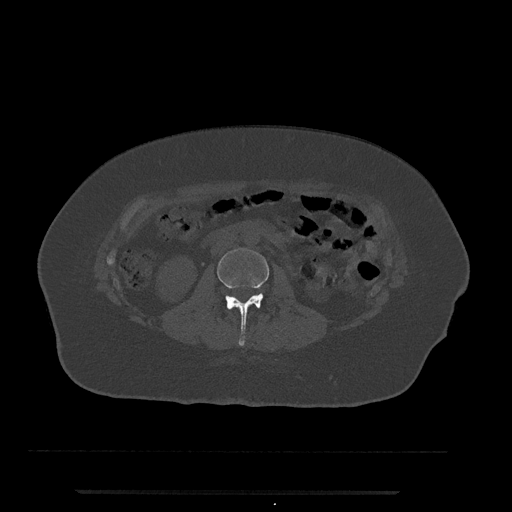
CT including the spine, one axial slice; slice 29 of 797 in the series (ordered by position); reconstruction kernel Br40s/3; 120 kVp; bone window (W 1800 / L 400 HU); 0.5 mm slice thickness; 512 × 512 image matrix, field of view 440 × 440 mm. Patient: female, 51 years. From the clinical record (not read from this slice): primary cancer: neuro; vertebrae with lytic lesions (as recorded): T8.
Structures marked on this image (semi-automatically segmented with operator editing):
- L2 vertebra: box from (x=217, y=248) to (x=269, y=346) px